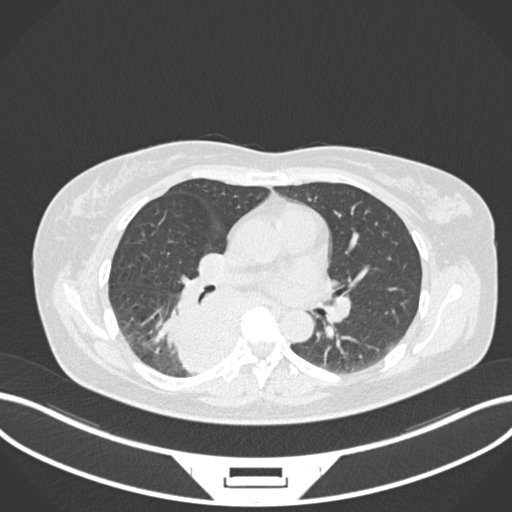
Chest CT, one axial slice. Position 595 of 677 along the scan axis. Reconstruction kernel B30f. 120 kVp. Lung window (W 1500 / L -600 HU). 1 mm slice thickness. 512 × 512 image matrix, field of view 400 × 400 mm. Patient: female, 54 years. From the clinical record (not read from this slice): clinical TNM (as recorded): T4 N0 M0.
Outlined on this slice (rectangle marked by the reading radiologist):
- lung tumour (recorded histology: adenocarcinoma): bounding box [x1, y1, x2, y2] px = [155, 278, 249, 375]